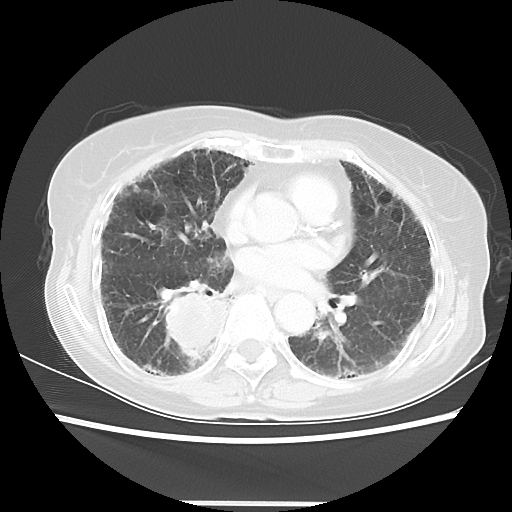
Chest CT, one axial slice. Slice 26 of 52 in the series (ordered by position). Lung window (W 1500 / L -600 HU). 5 mm slice thickness. 512 × 512 image matrix. Female patient, age 71 years. Case-level facts recorded for this patient, not image findings: clinical TNM (as recorded): T3 N0 M0.
Outlined on this slice (bounding box drawn by a radiologist):
- lung tumour (recorded histology: squamous cell carcinoma): box from (x=160, y=280) to (x=232, y=369) px